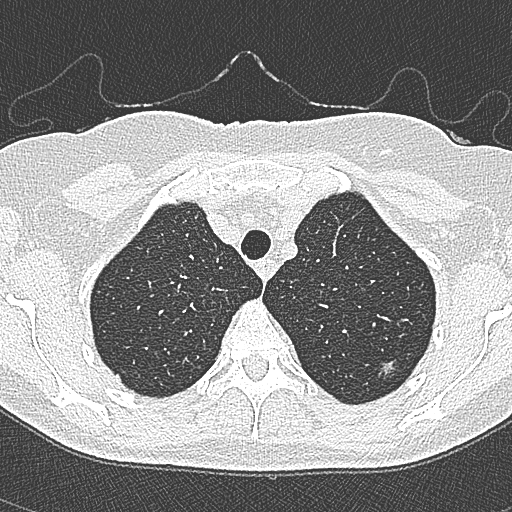
Low-dose screening chest CT, axial slice. Second annual screen. Lung window (W 1500 / L -600 HU). 1 mm slice thickness. Slice 51 of 350 in the series. Female, age 65 years at enrolment.
- Expert reader's lesion annotation, bounding box [x1, y1, x2, y2] px = [367, 348, 410, 387].
- The screening reader recorded 4 non-calcified nodules or masses ≥4 mm on this exam; which of them this box marks is not recorded.
- Later outcome: lung cancer diagnosed 54 days after this screen — bronchiolo-alveolar carcinoma, non-mucinous, left upper lobe, stage IA (AJCC 6th edition), 10 mm at pathology.